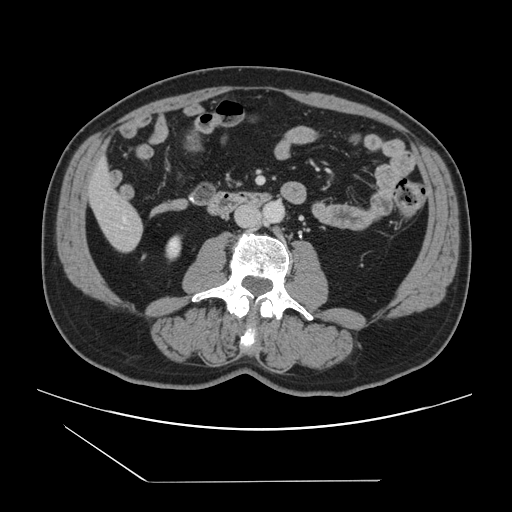
Contrast-enhanced abdominal CT, one axial slice; position 23 of 157 along the scan axis; 120 kVp; intravenous contrast given; soft-tissue window (W 400 / L 40 HU); 2.5 mm slice thickness; 512 × 512 image matrix, field of view 407 × 407 mm. Male patient, age 61 years. From the clinical record (not read from this slice): diagnosis: colorectal cancer liver metastases, imaged before liver resection; multiple liver metastases: yes; largest metastasis: 5.5 cm; chemotherapy before resection: no.
Outlined on this slice (manually delineated by an expert):
- liver: bounding box <90,163,143,251> (left, top, right, bottom; pixels)
- planned liver remnant (the part of the liver to remain after resection): <90,162,133,218>